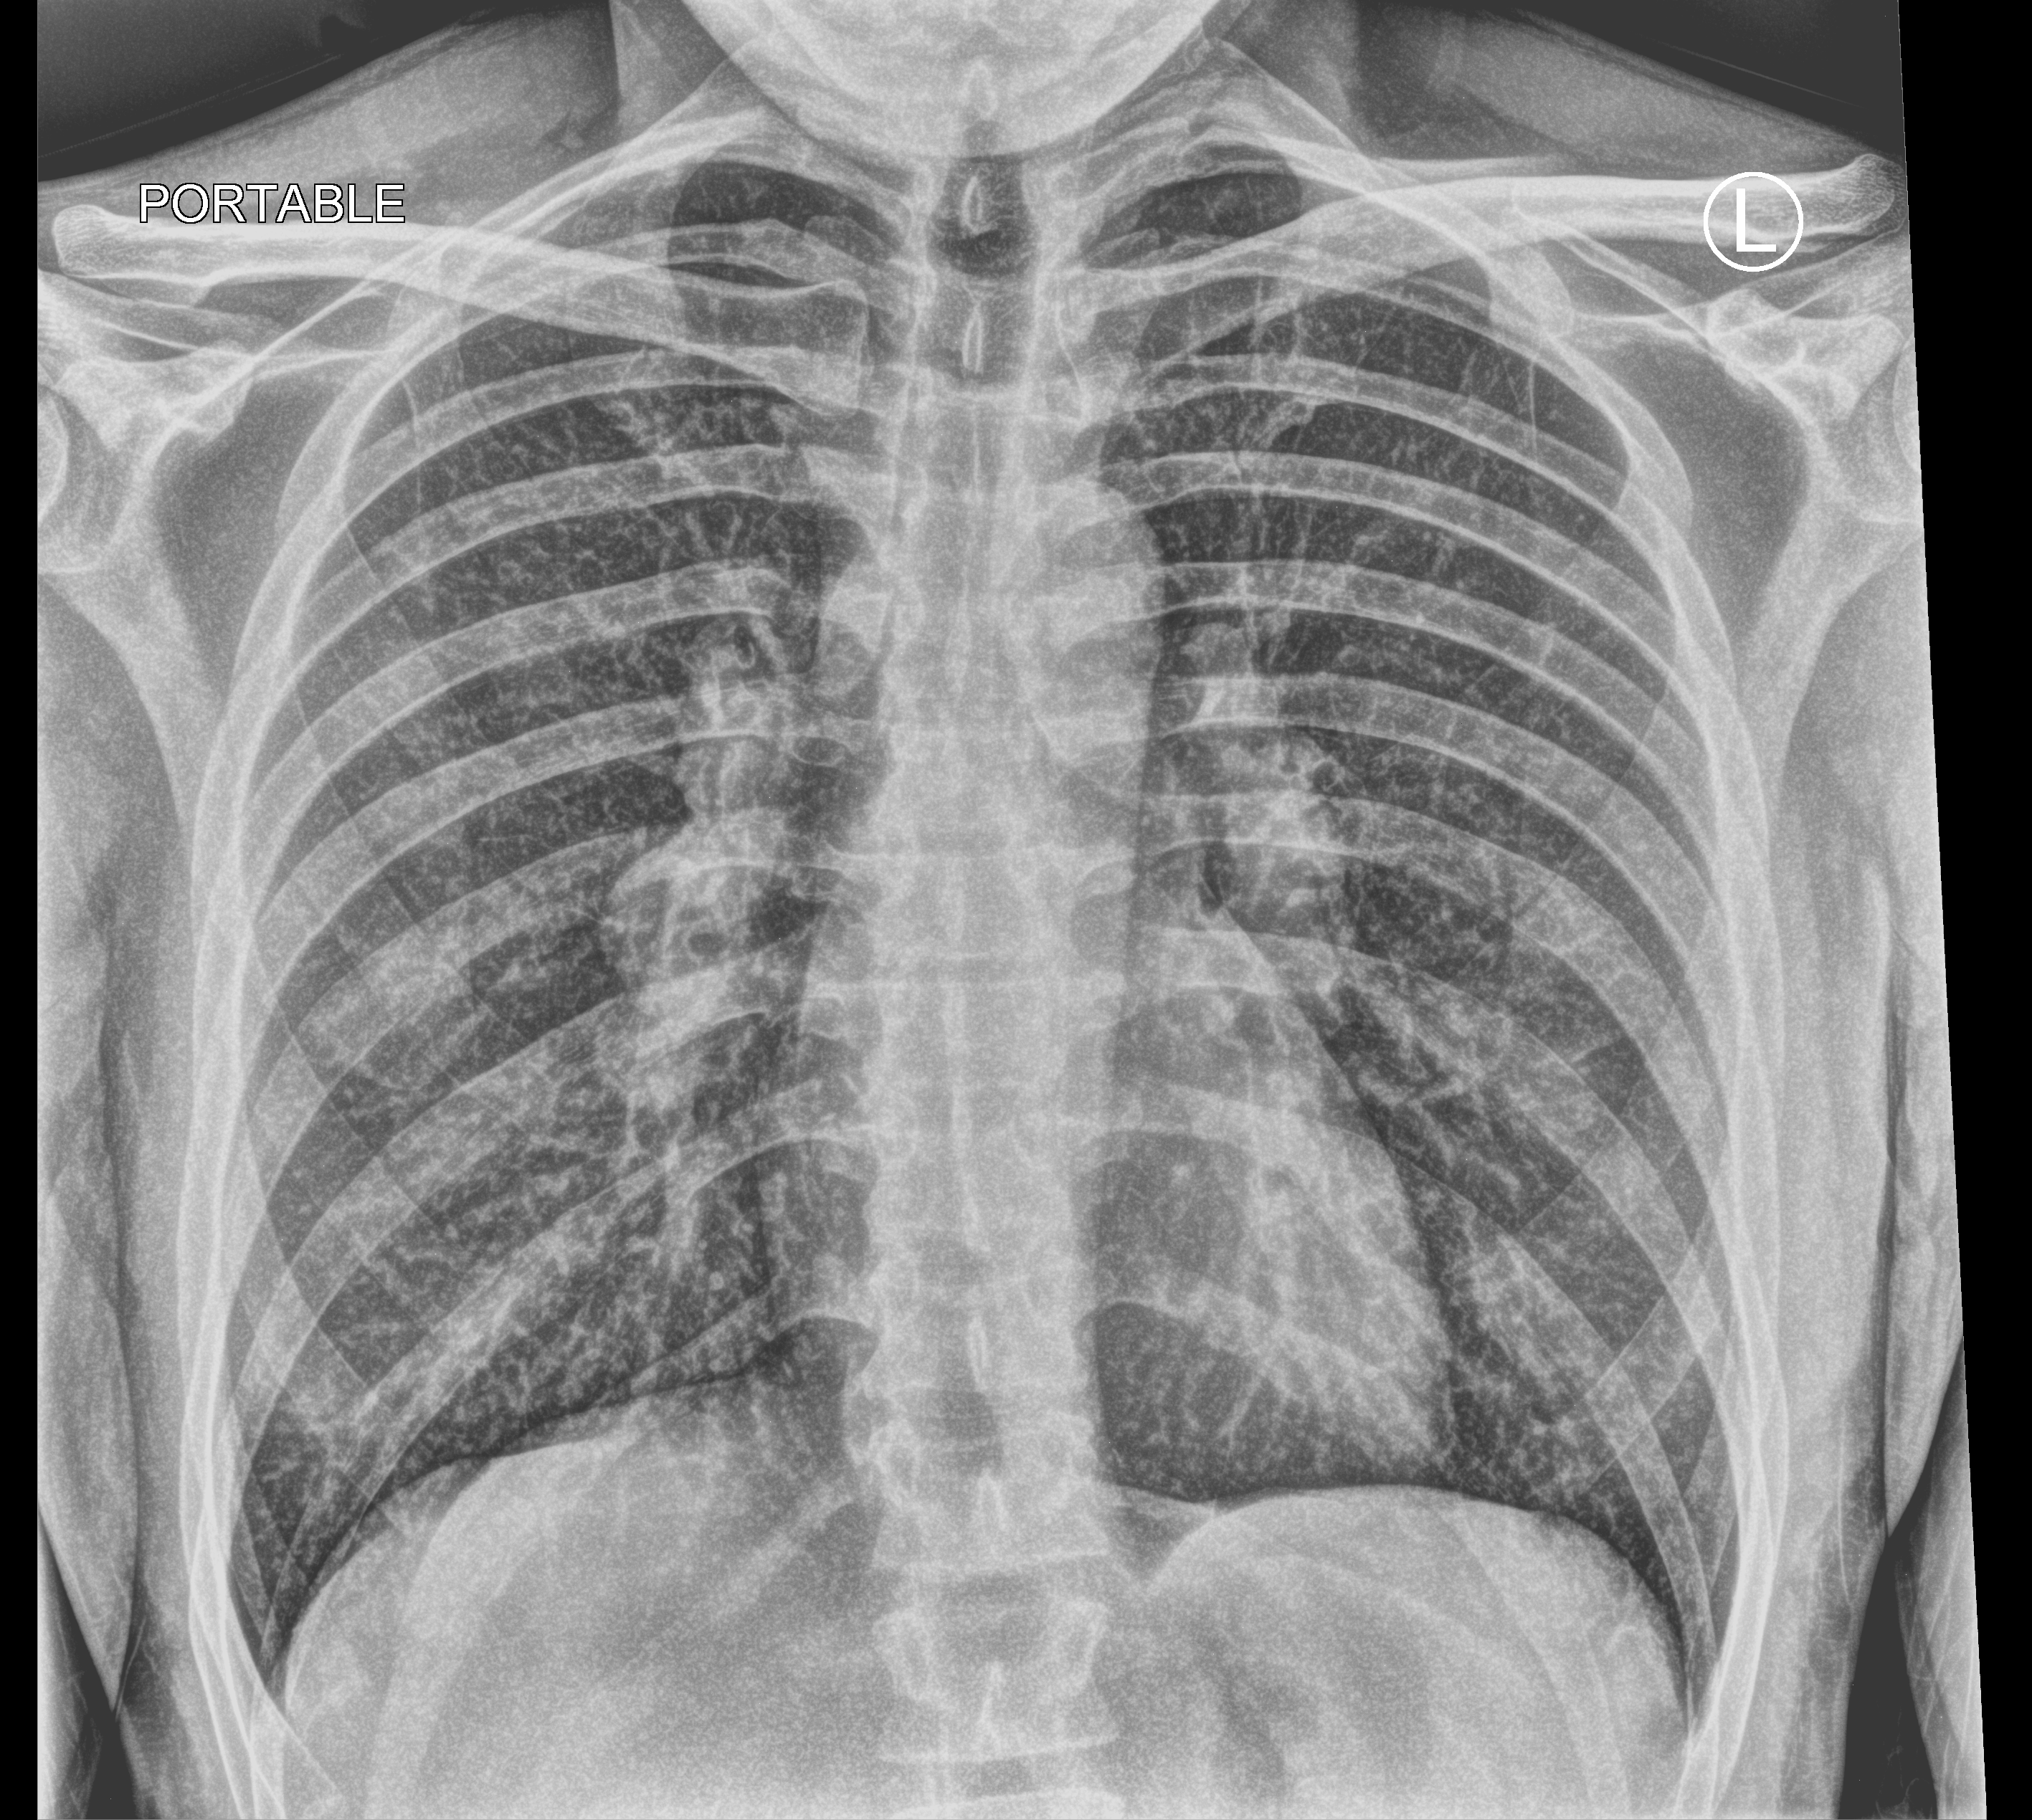
Portable chest radiograph; anteroposterior (AP) projection. Male patient hospitalised with COVID-19, age 18–59 years.
Admission-level facts for this patient (not findings on this image; timing relative to this image not recorded): admitted to intensive care during this hospital stay: no; mechanically ventilated during this hospital stay: no.